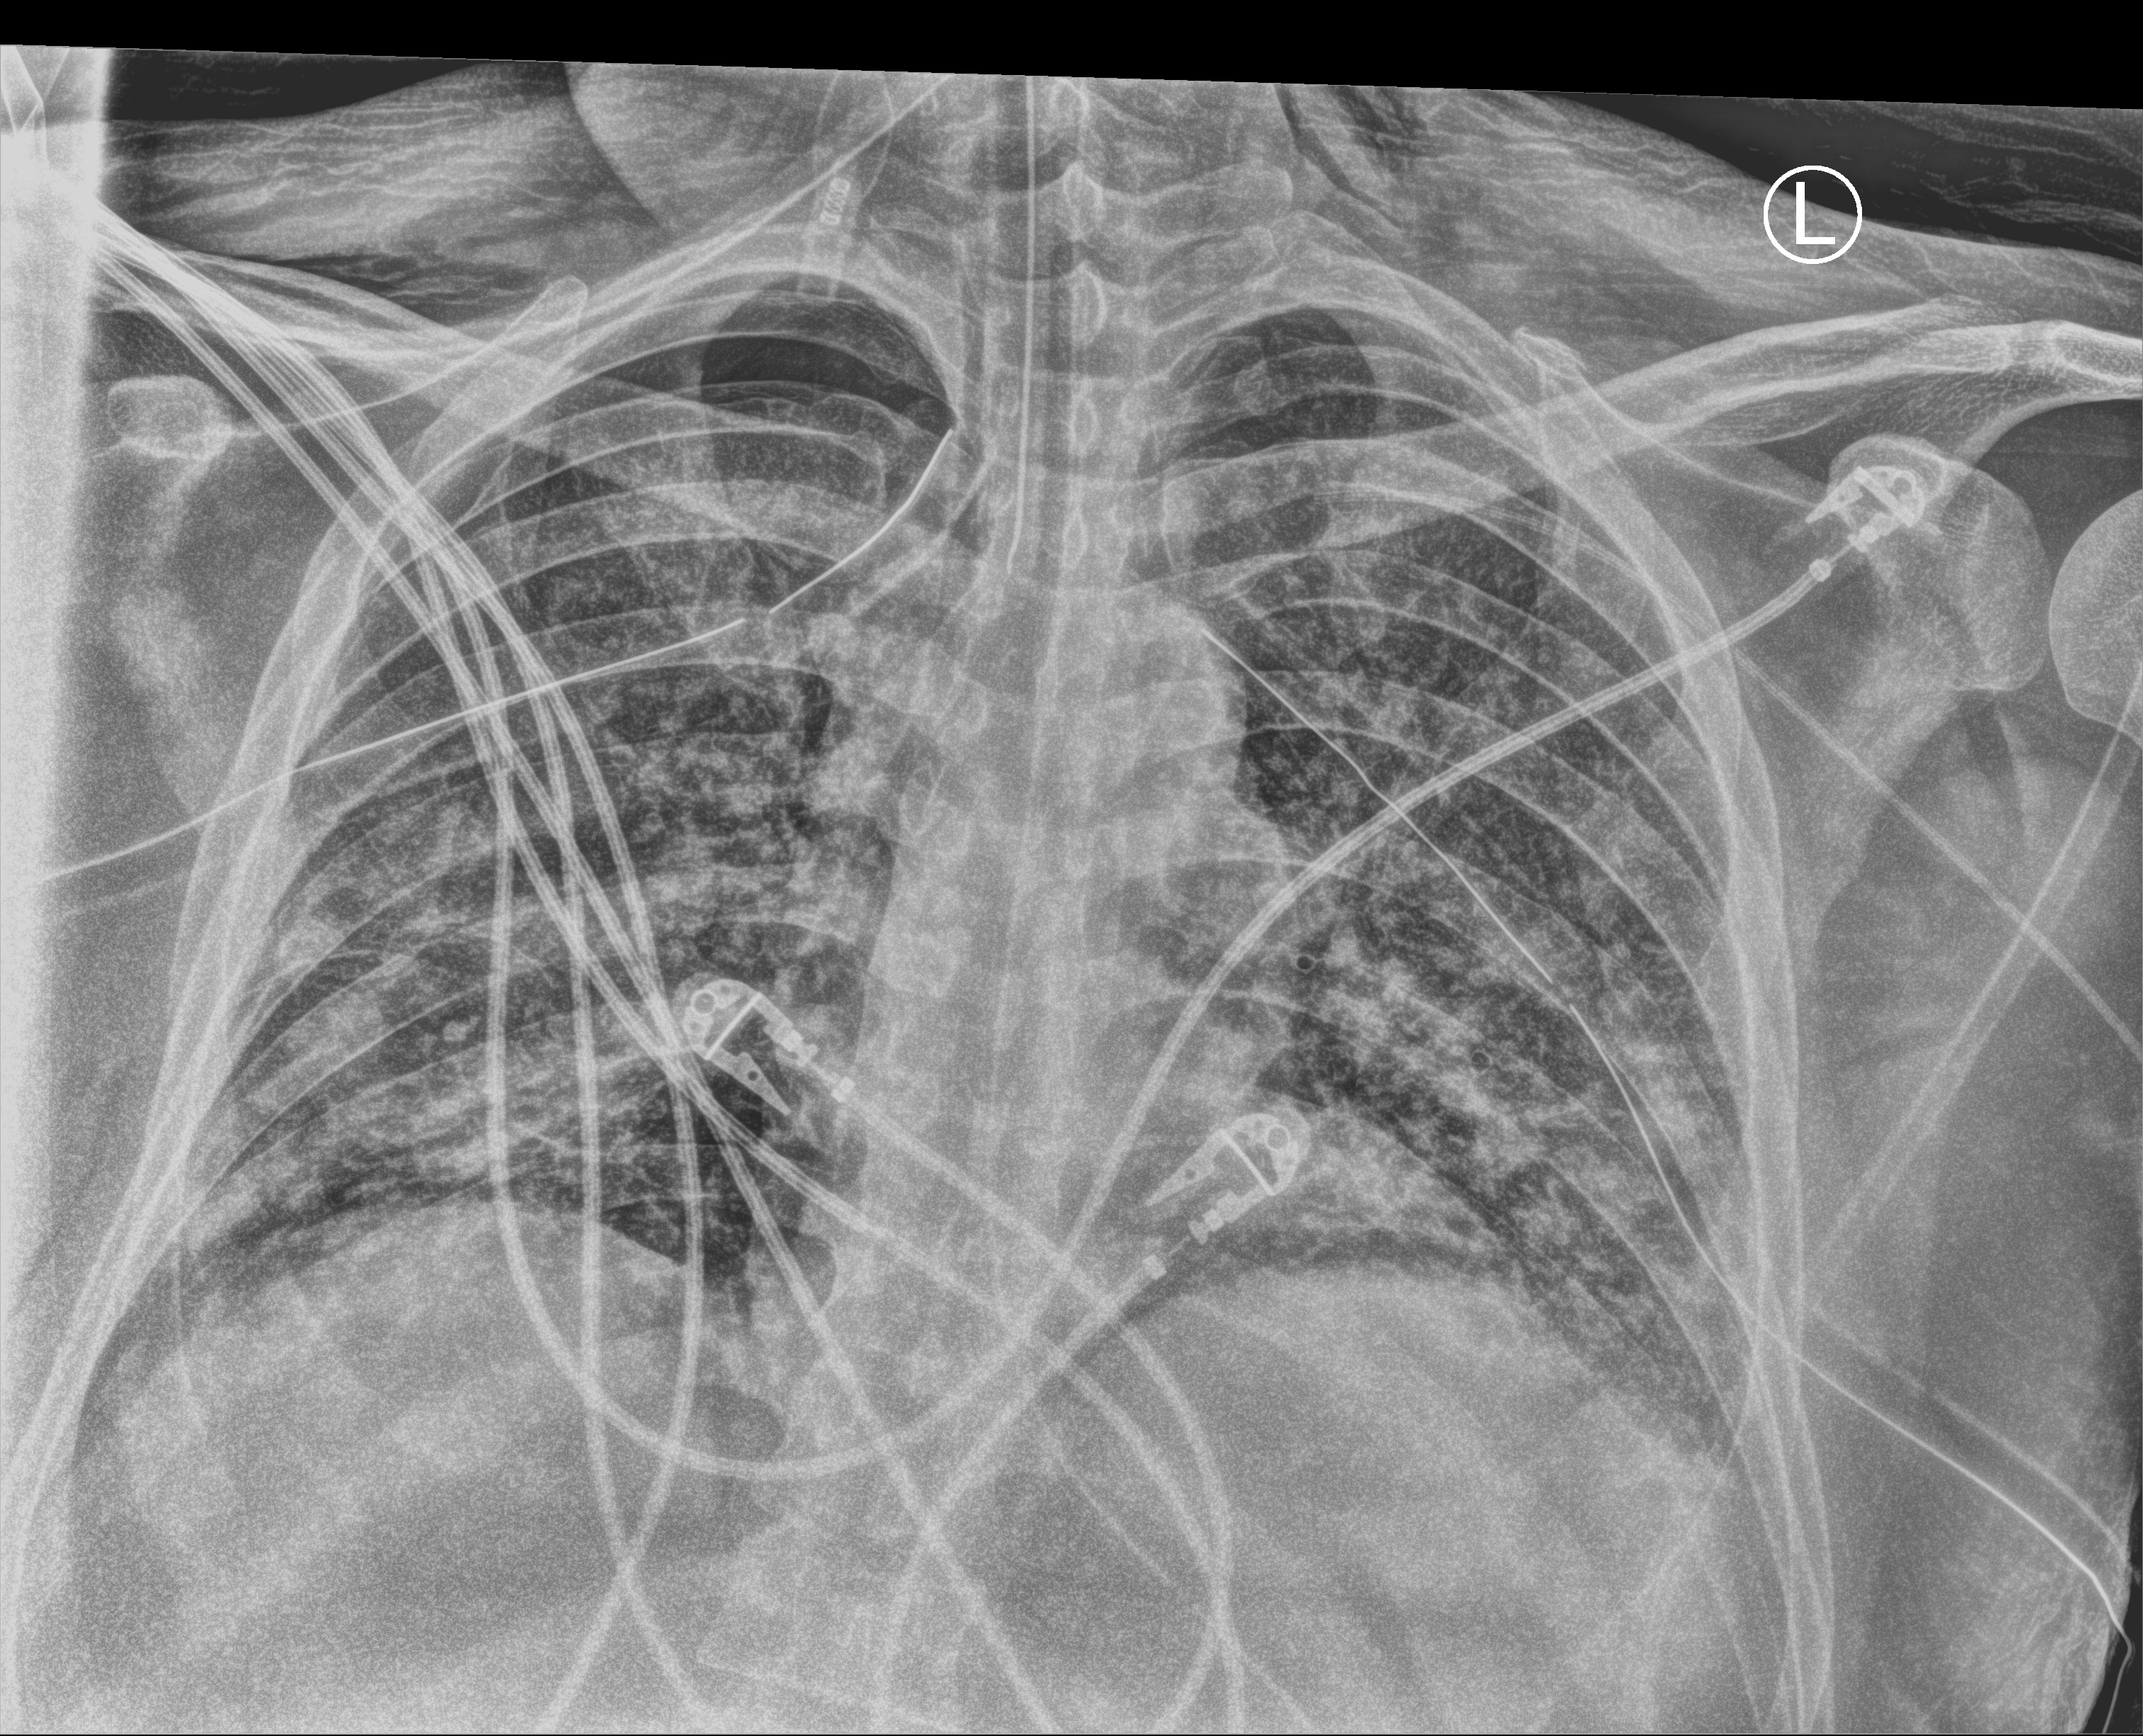
Chest X-ray (portable), anteroposterior (AP) projection. Male patient hospitalised with COVID-19, age 18–59 years.
Hospital-stay facts (about this admission, not read from this image; timing relative to this image not recorded): mechanically ventilated during this hospital stay: yes.